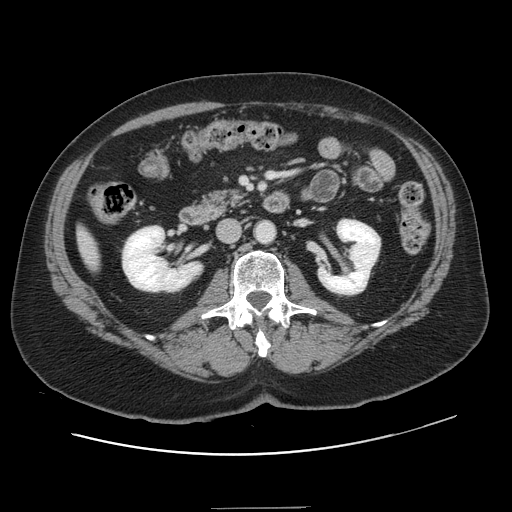
Contrast-enhanced abdominal CT, one axial slice; position 46 of 143 along the scan axis; 120 kVp; intravenous contrast given; soft-tissue window (W 400 / L 40 HU); 512 × 512 image matrix, field of view 402 × 402 mm. Male patient, age 62 years. Case-level facts recorded for this patient, not image findings: diagnosis: colorectal cancer liver metastases, imaged before liver resection; multiple liver metastases: yes; largest metastasis: 2.7 cm; chemotherapy before resection: yes.
Outlined on this slice (expert manual segmentation):
- liver: bounding box (x1, y1, x2, y2) in pixels: (79, 231, 98, 267)